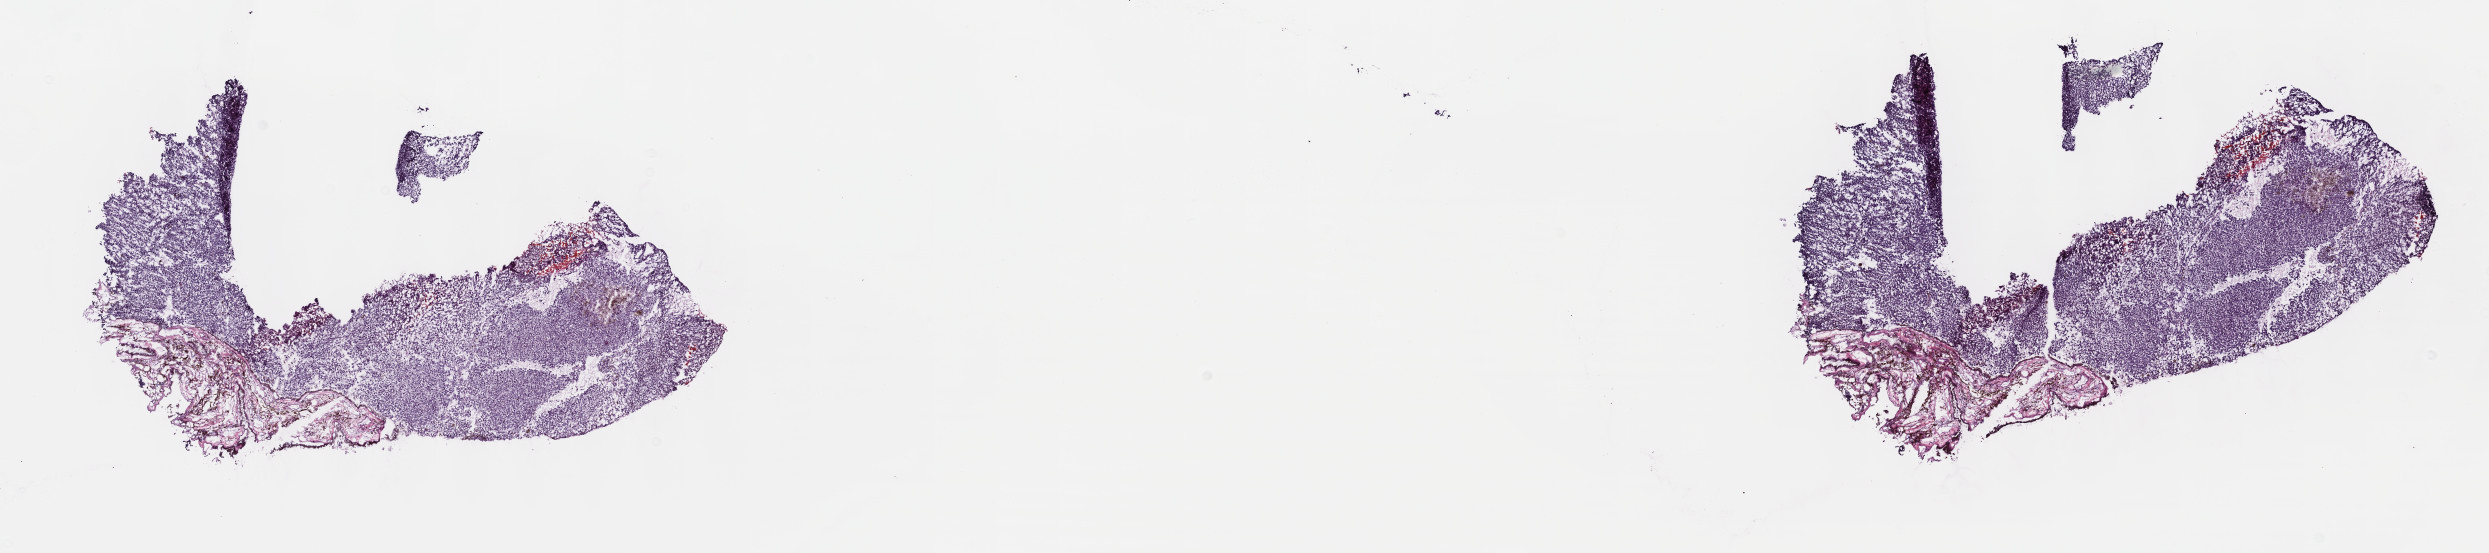
Digitized H&E tissue section (whole slide) — whole scanned area (about 20.1 x 4.5 mm, acquisition: 40x scan) shown as a low-resolution overview; frozen section from the top of the tissue portion; sample: primary tumour, uvea. Female, age 50 years at initial diagnosis.
Diagnosis: Mixed epithelioid and spindle cell melanoma (choroid).